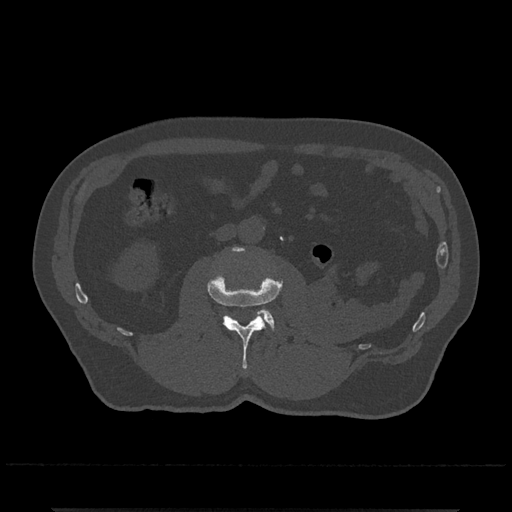
CT including the spine, one axial slice. Position 276 of 797 along the scan axis. Reconstruction kernel Br40s/3. 120 kVp. Bone window (W 1800 / L 400 HU). 0.5 mm slice thickness. 512 × 512 image matrix. Patient: male, 67 years. From the clinical record (not read from this slice): primary cancer: prostate.
Outlined on this slice (semi-automatically segmented with operator editing):
- L2 vertebra: bounding box (x1, y1, x2, y2) in pixels: (207, 247, 282, 369)
- L3 vertebra: (258, 310, 275, 329)